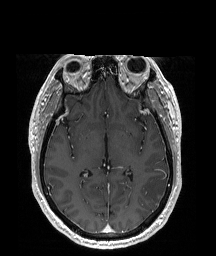
Brain MRI from a brain-tumour surgery series, one axial slice. Position 103 of 192 along the scan axis. T1-weighted post-contrast. 1 mm slice thickness. 216 × 256 image matrix, field of view 219 × 260 mm. From the clinical record (not read from this slice): histopathology: Glioblastoma; WHO grade: 4; IDH mutation: no; tumour location: Left Temporal Parietal.
Outlined on this slice (expert manual segmentation):
- tumour: bounding box [x1, y1, x2, y2] px = [141, 176, 168, 205]